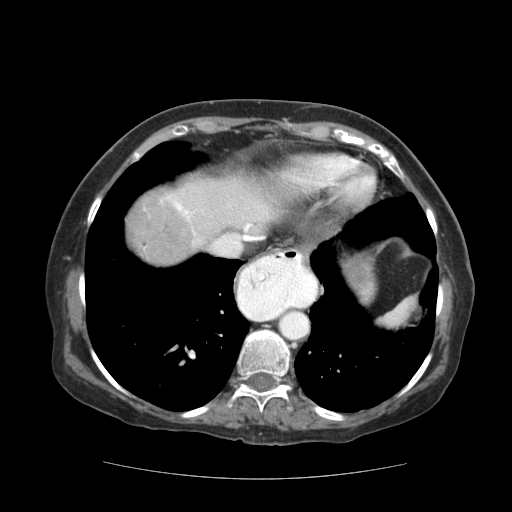
Contrast-enhanced abdominal CT (liver protocol), one axial slice; reconstruction kernel STANDARD; 140 kVp; soft-tissue window (W 400 / L 40 HU); 2.5 mm slice thickness; 512 × 512 image matrix, field of view 360 × 360 mm. Case-level facts recorded for this patient, not image findings: diagnosis: hepatocellular carcinoma (patient treated with transarterial chemoembolisation; whether this scan precedes or follows treatment is not stated here); TNM stage (as recorded): Stage-I; Child-Pugh class: A; tumour nodularity: uninodular.
Outlined on this slice (semi-automatic segmentation, software-assisted and operator-edited):
- abdominal aorta: bounding box <279,311,308,339> (left, top, right, bottom; pixels)
- liver parenchyma outside the tumour (the mass and vessels are separate outlines, so this box may not span the whole liver): <128,176,276,264>
- mass: <134,201,189,261>
- liver vessels: <168,196,260,240>